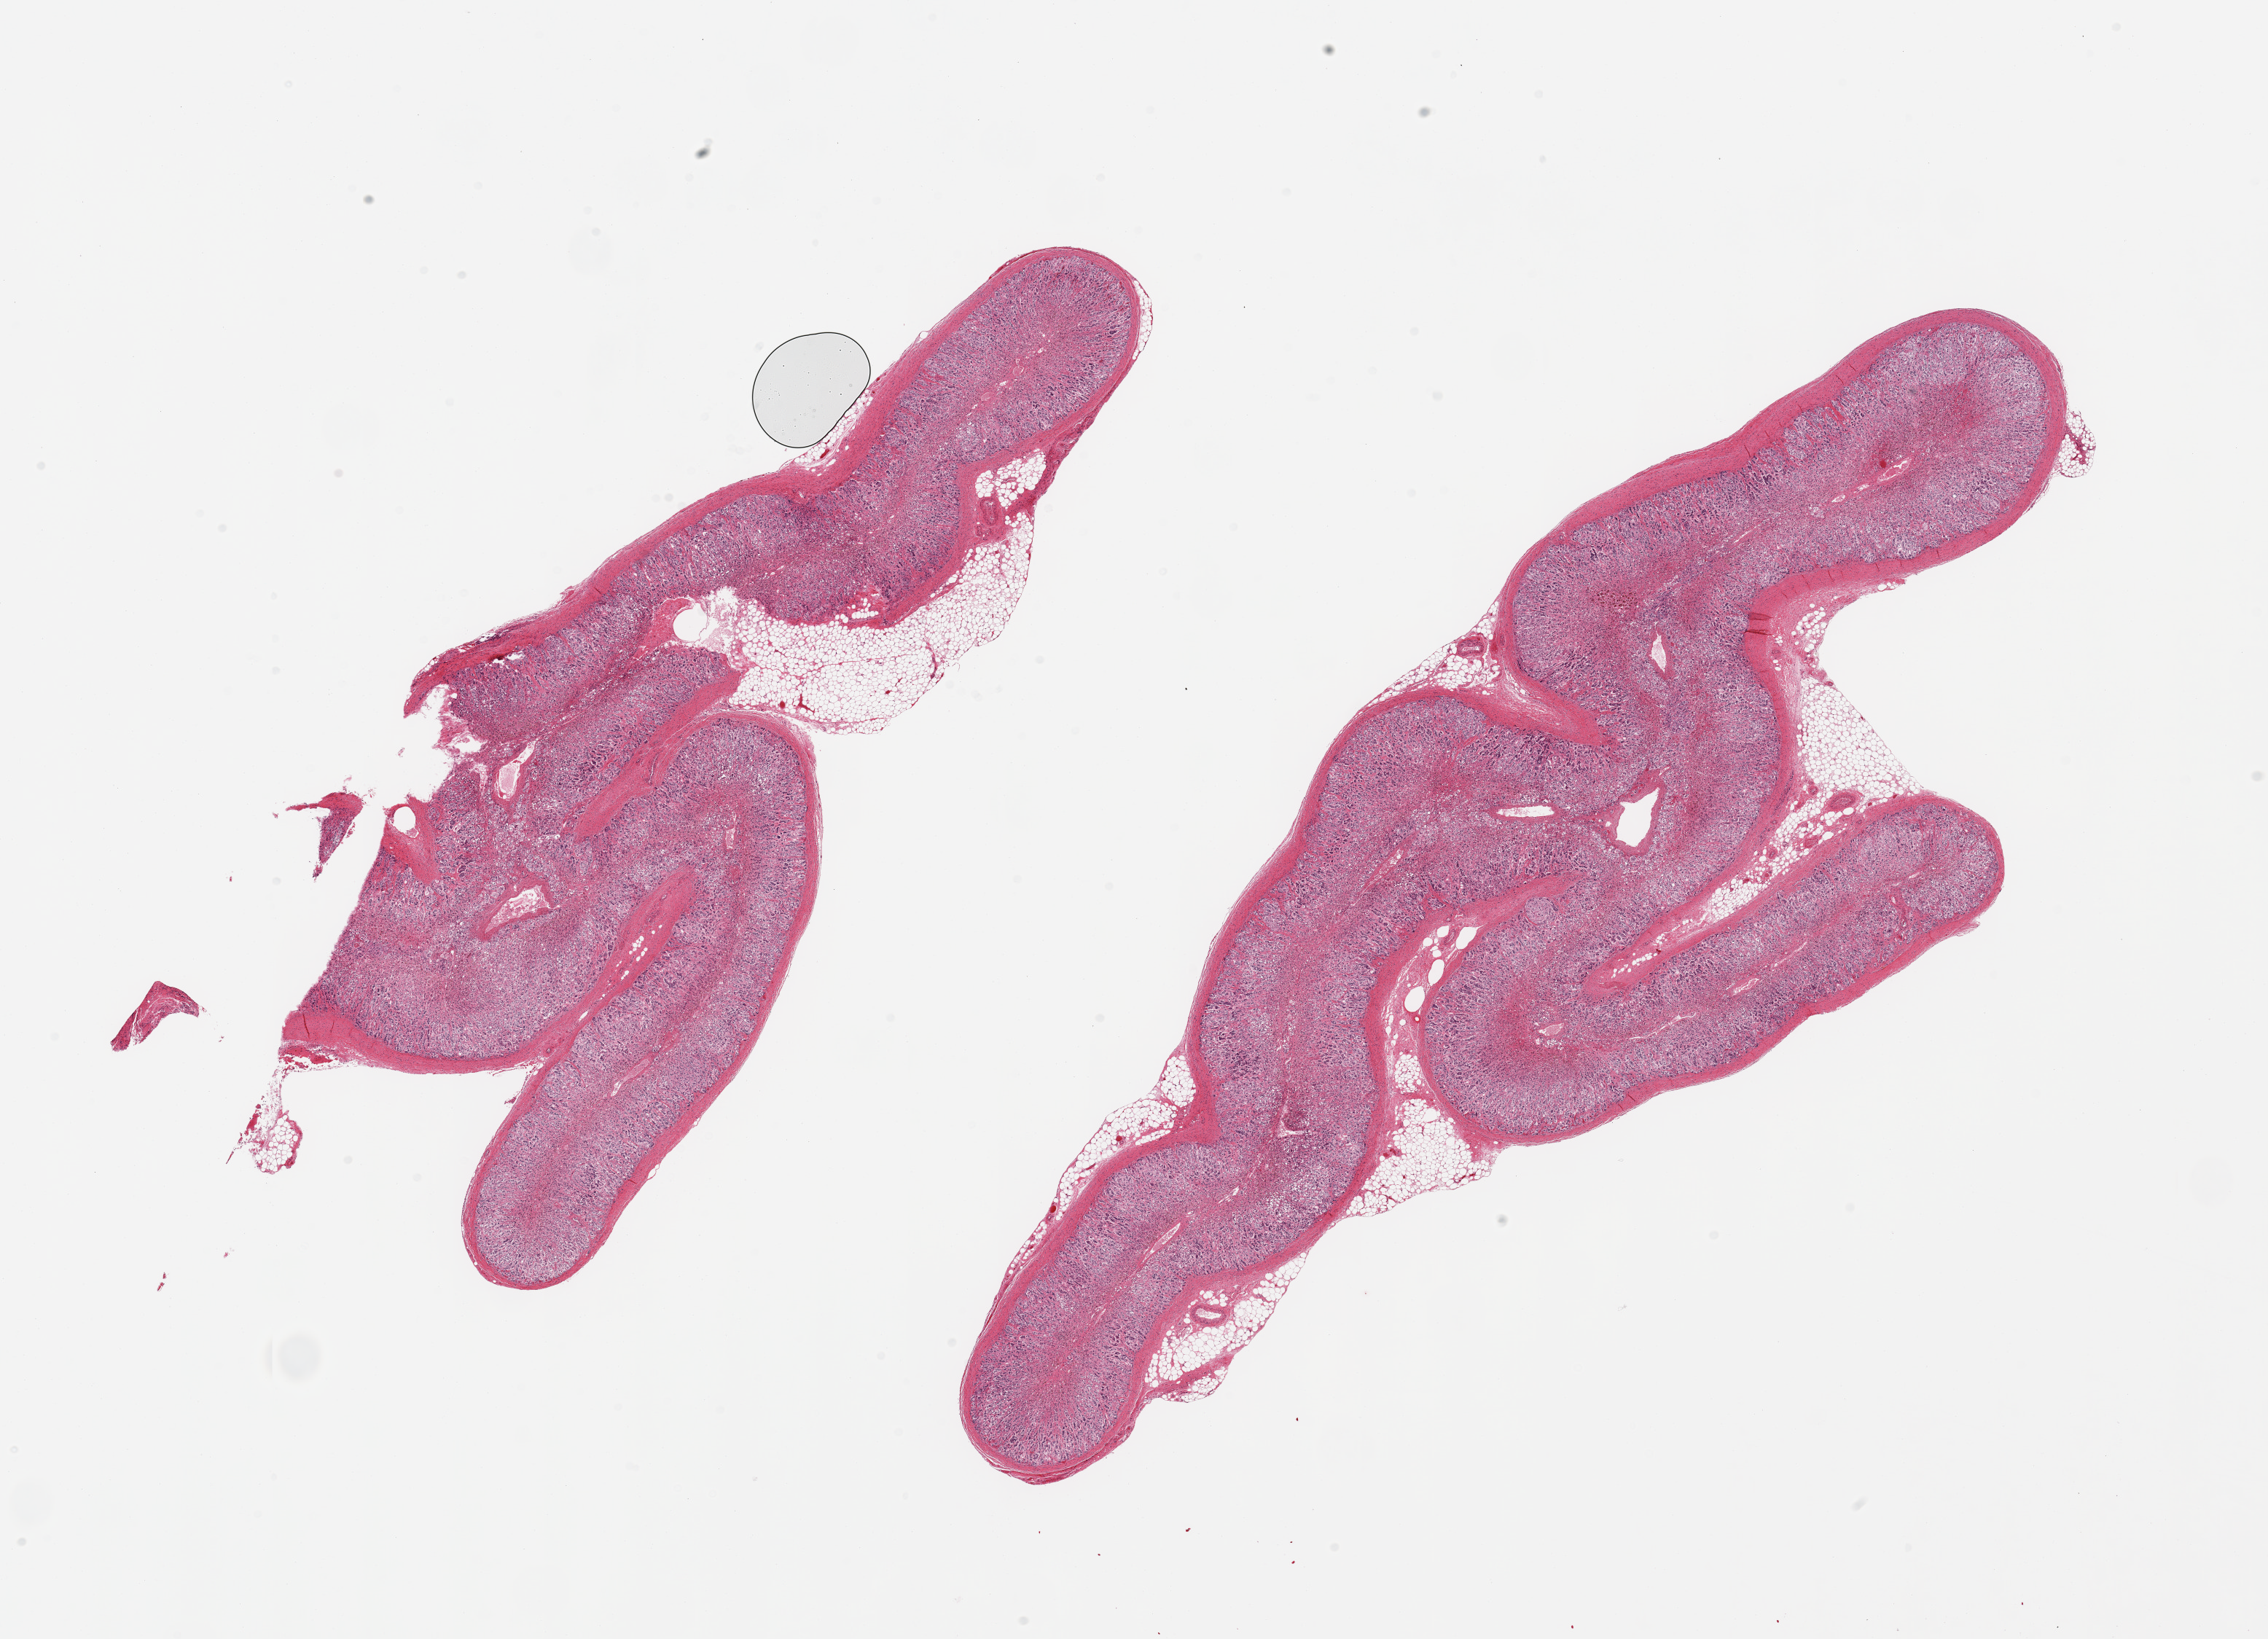
Whole-slide image, H&E stain, a low-resolution overview of the entire scanned area, about 24.6 x 17.8 mm. PAXgene-fixed paraffin-embedded (PFPE) section. Target tissue: adrenal gland. Donor tissue sample. Donor: female.
Pathologist's review note for this sample: 2 pieces; well dissected, with 10% external fat.